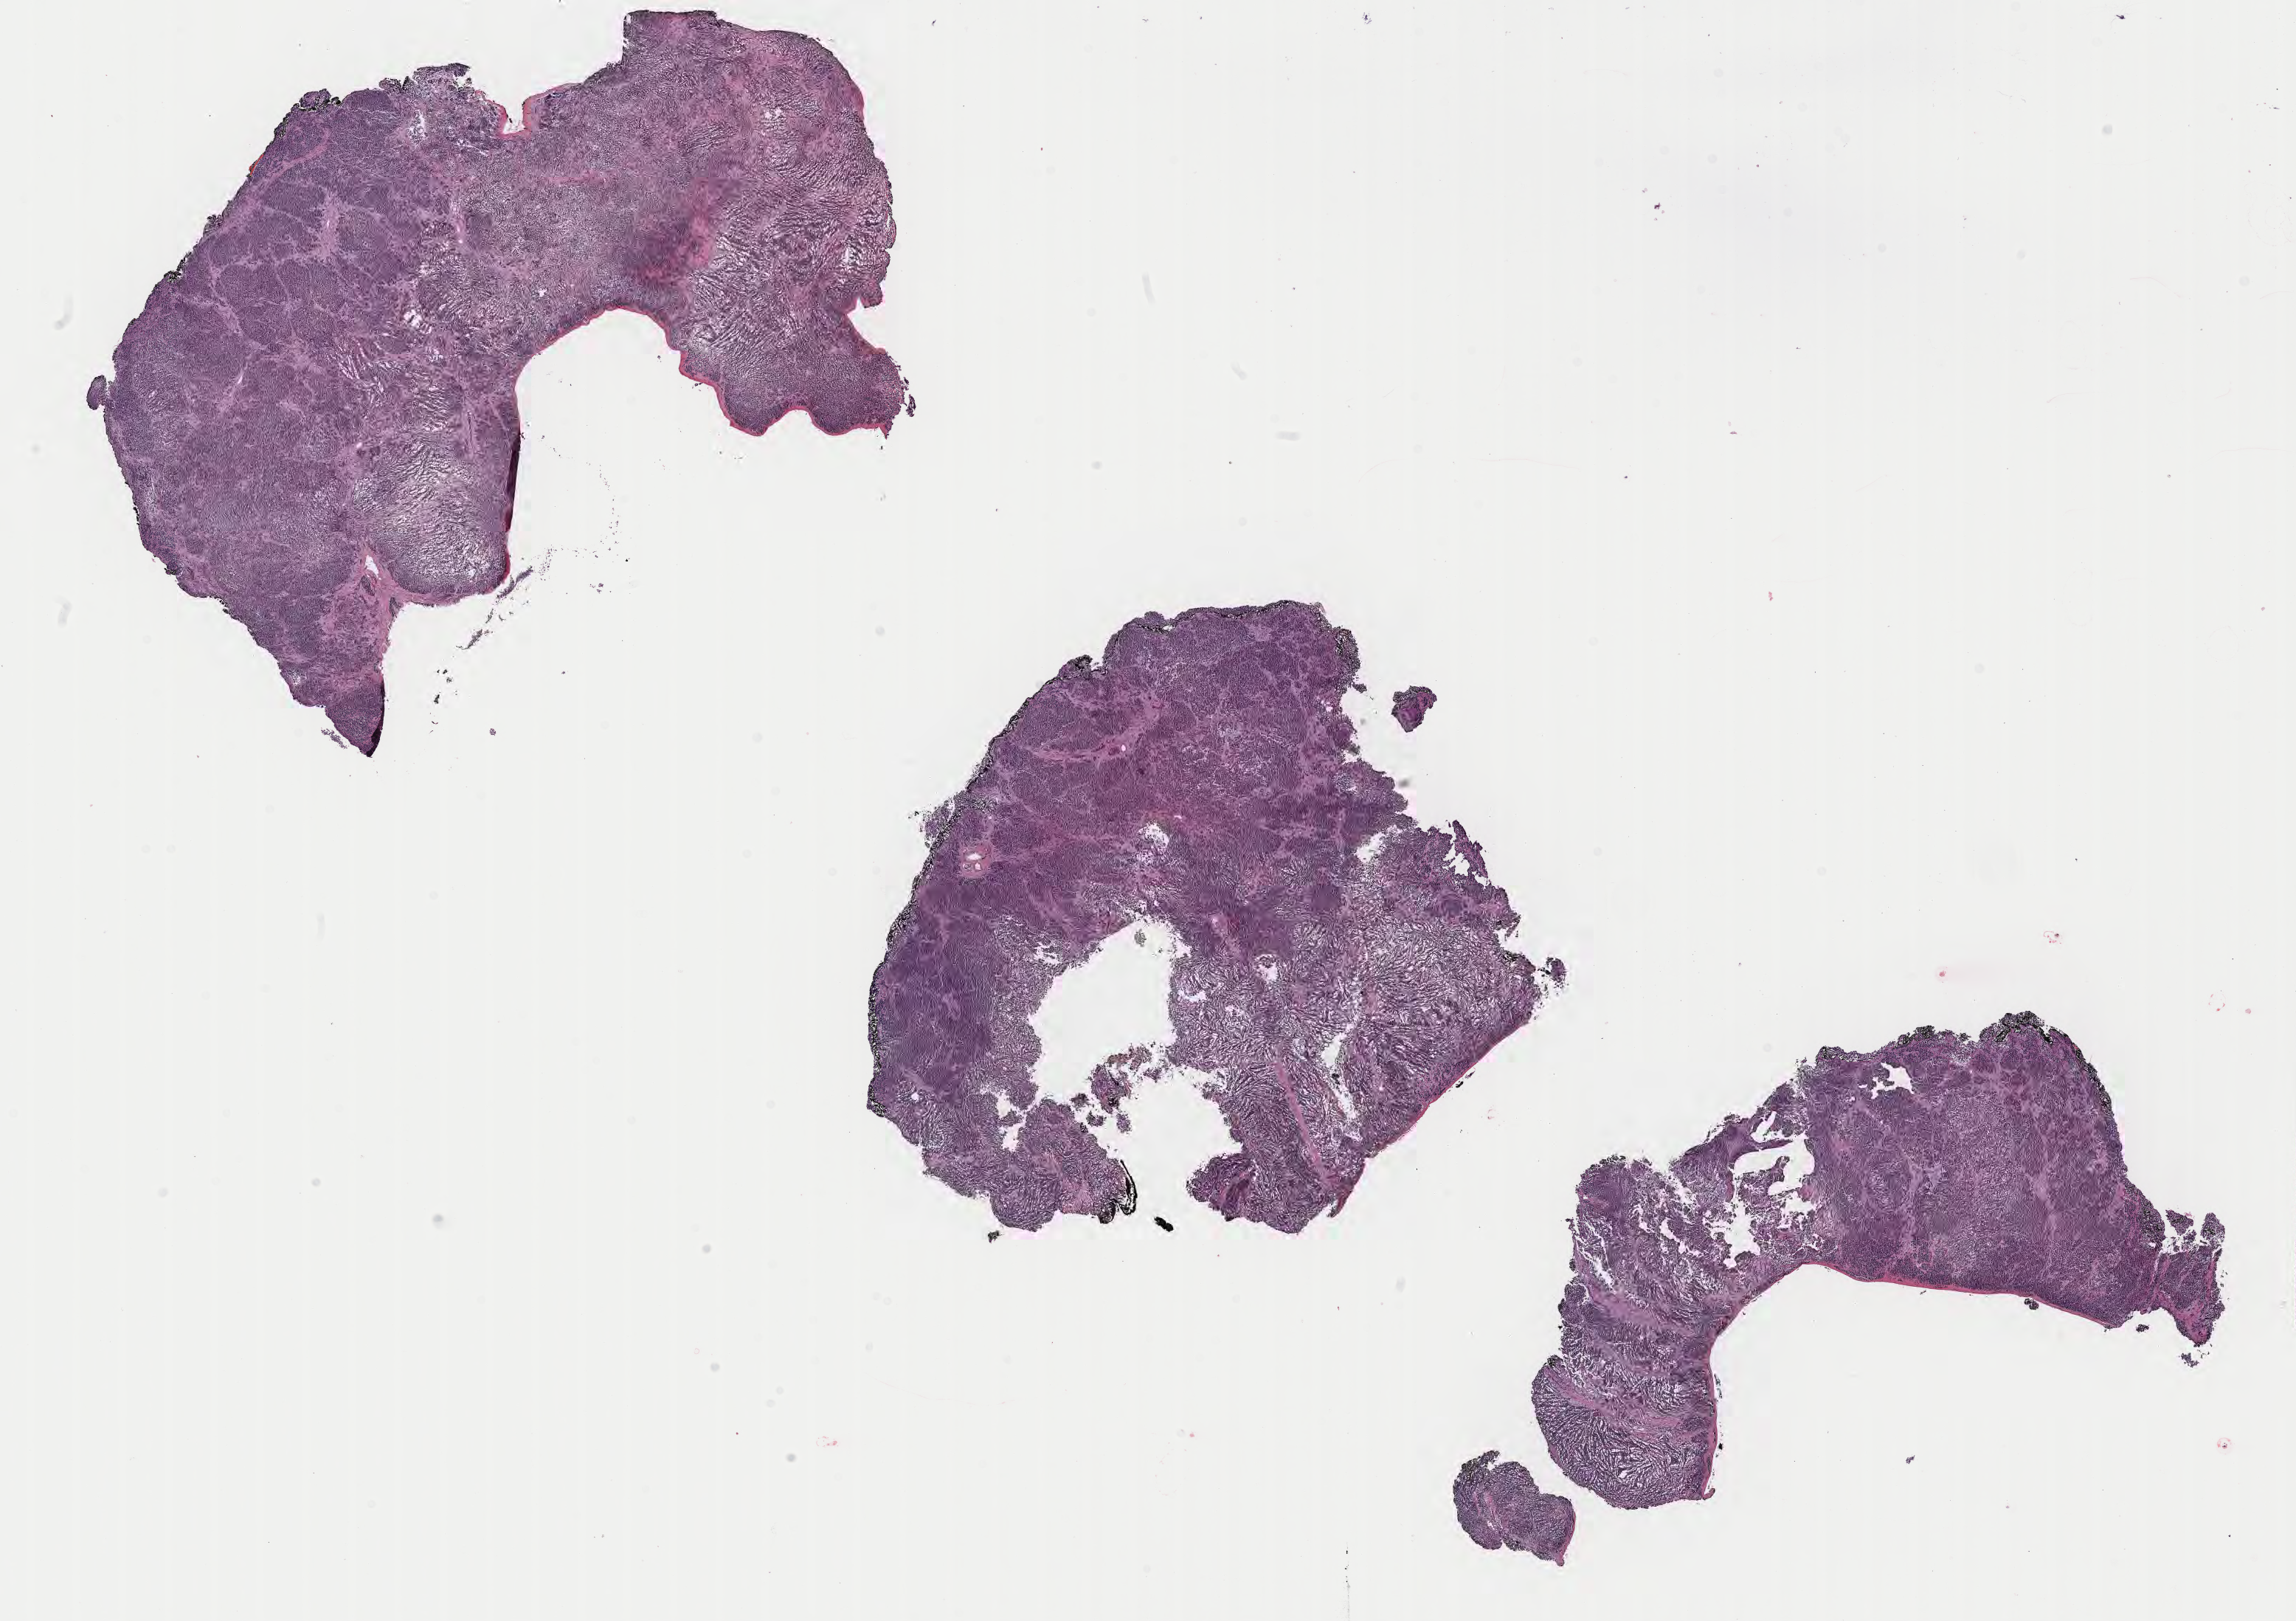
H&E whole-slide image of tumor tissue from the liver, a low-resolution overview of the entire scanned area, about 25.2 x 17.8 mm; formalin-fixed, paraffin-embedded (FFPE) tissue. Patient male; age 168 days.
Recorded diagnosis: Neuroblastoma, NOS.